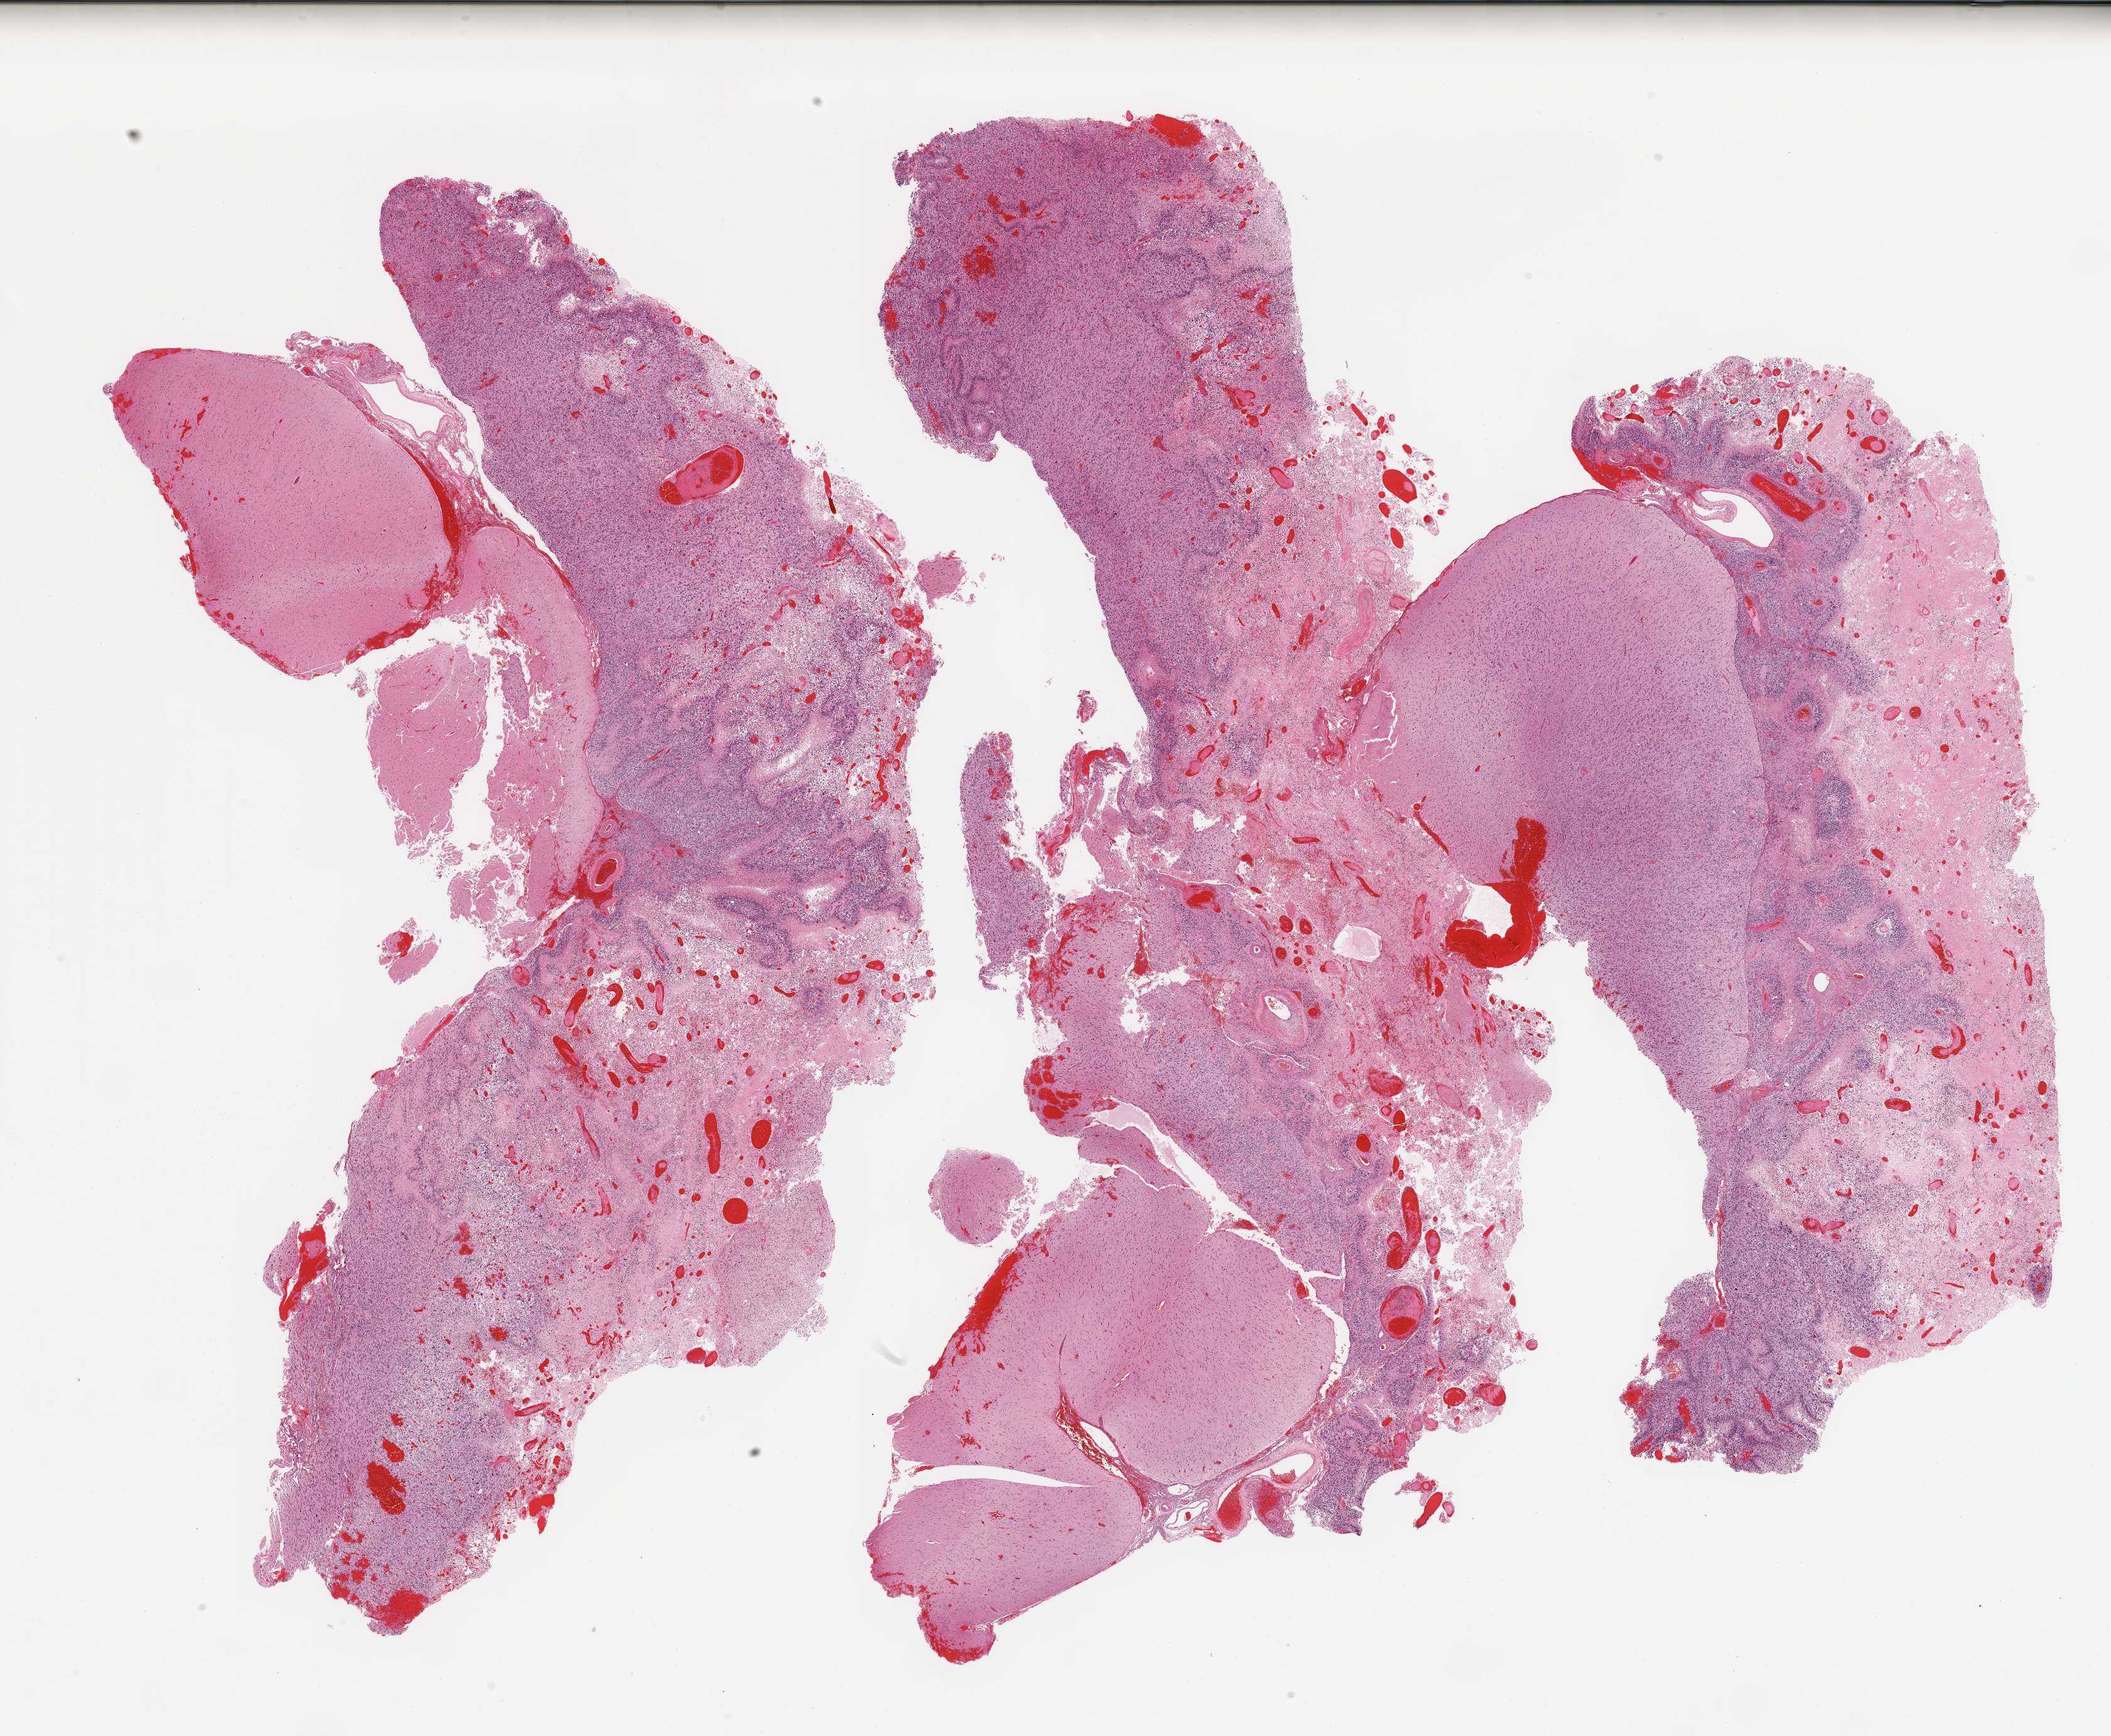
Whole-slide histology image, Hematoxylin and eosin (H&E) stained, shown as a low-resolution overview of the whole scanned area (about 26.6 x 21.9 mm, from a 20x scan); tumour tissue sample, brain. Male, 58 y/o.
Histologic diagnosis: Glioblastoma. Primary tumour site (as recorded): temporal lobe.